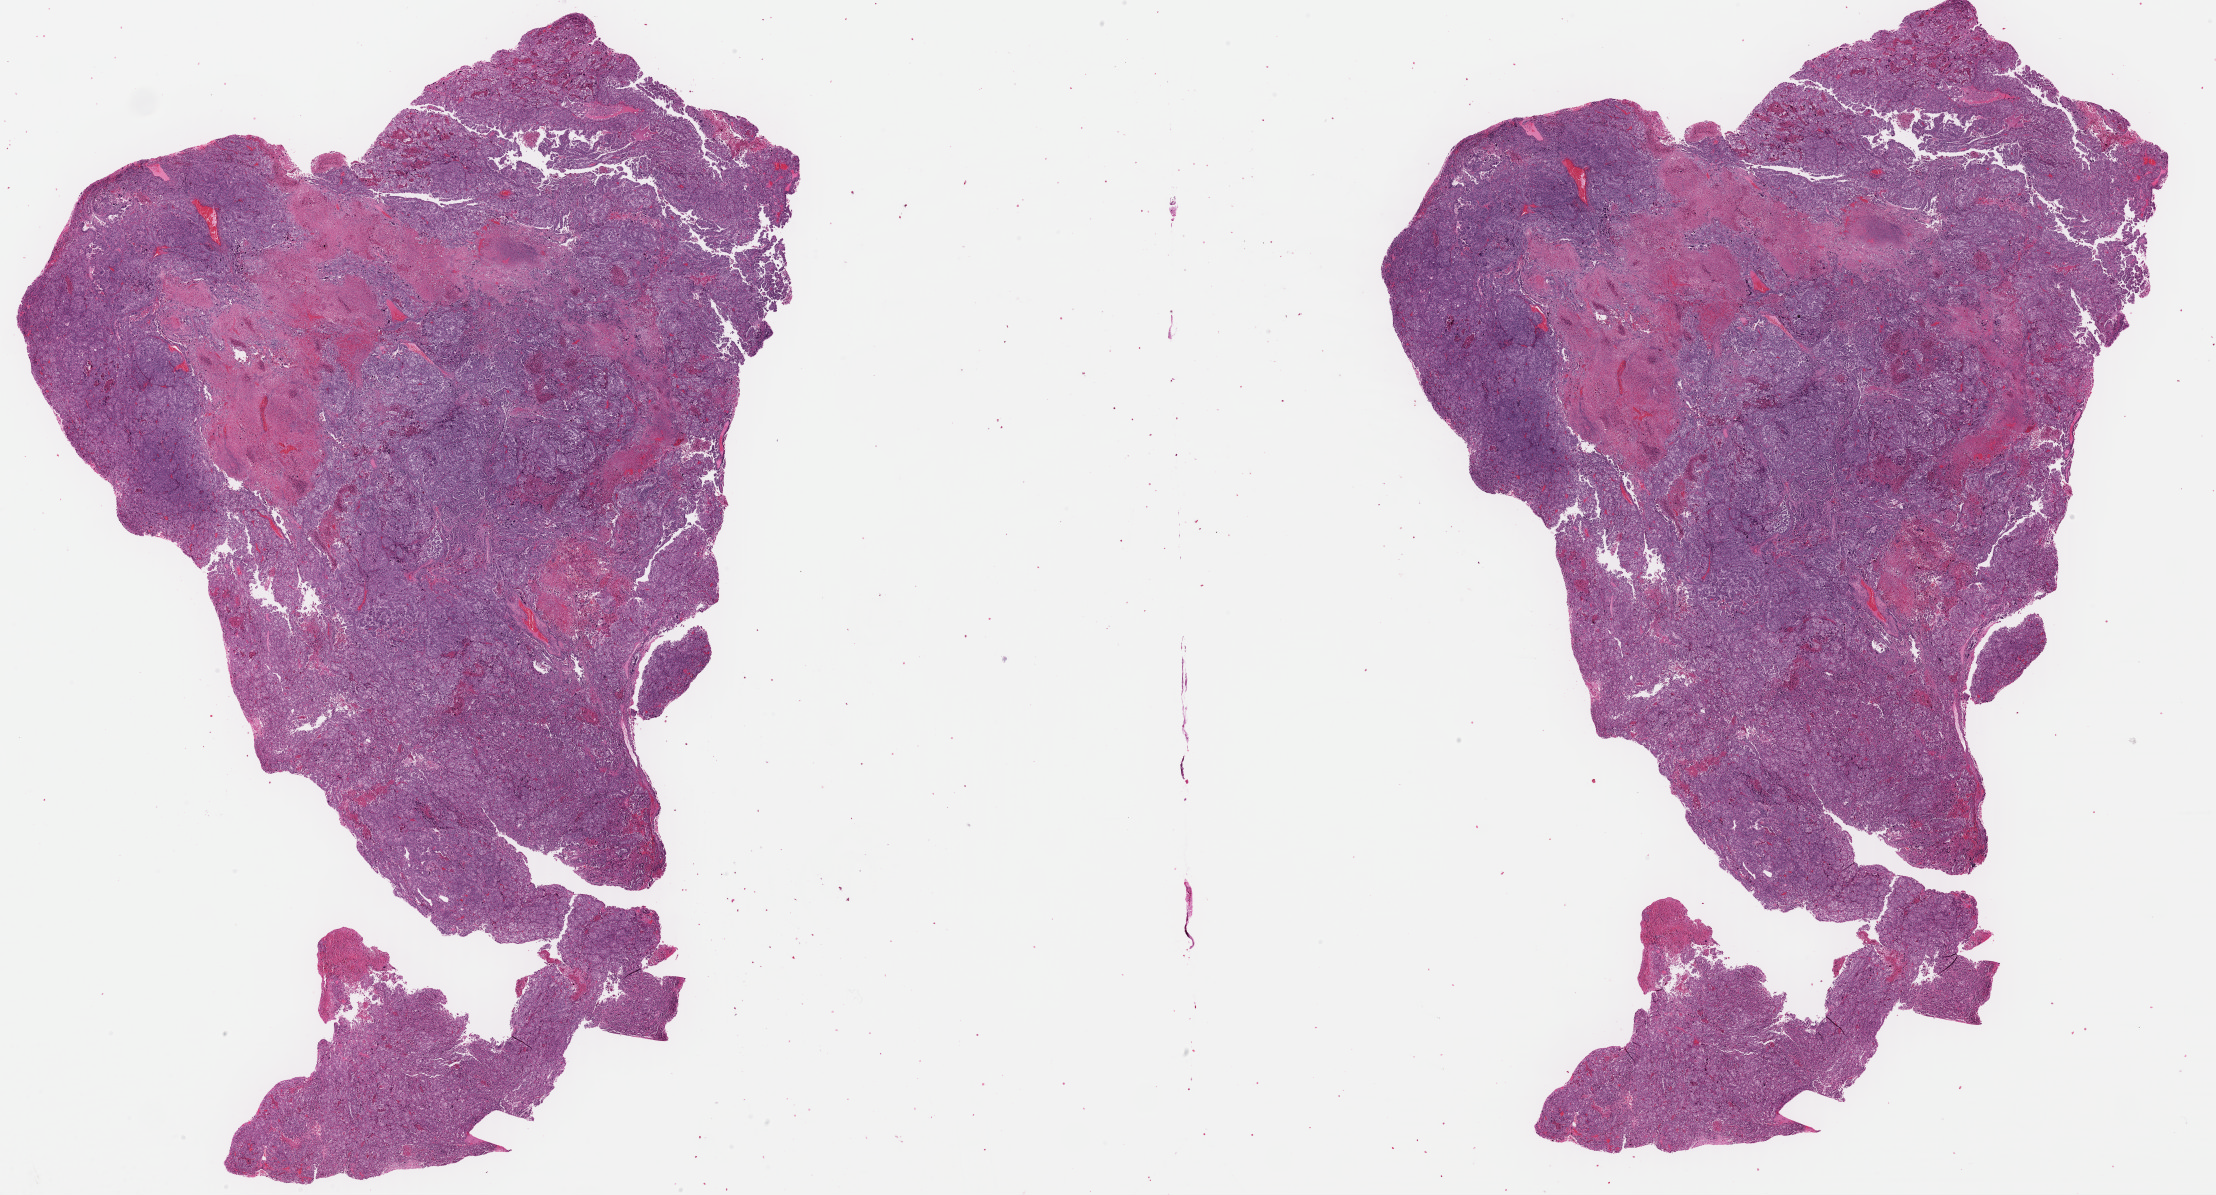
Hematoxylin and eosin (H&E) stained whole-slide image — a low-resolution overview of the entire scanned area, about 35.0 x 18.9 mm. Formalin-fixed paraffin-embedded (FFPE) diagnostic section. Primary tumour sample from the uterus. Patient: female, age at initial diagnosis 71 years. Histologic grade: G3 (poorly differentiated).
FIGO stage: IVB. Histologic diagnosis: Serous cystadenocarcinoma, NOS (endometrium).